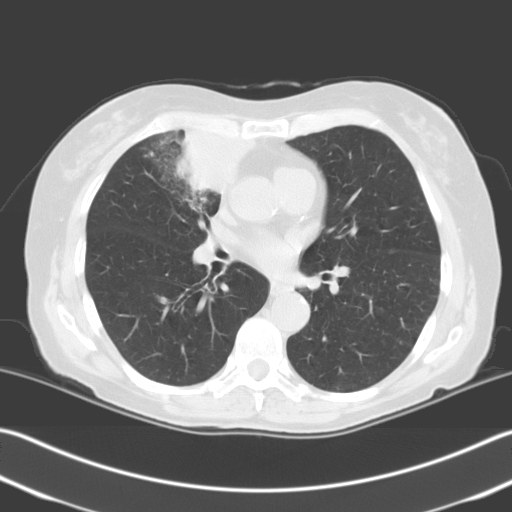
Low-dose screening chest CT, one axial slice; slice 116 of 204 in the series (ordered by position); lung window (W 1500 / L -600 HU); 3.2 mm slice thickness; 512 × 512 image matrix, field of view 348 × 348 mm.
Annotated regions visible in this slice (expert manual segmentation):
- lesion 1 (tumor, upper lobe of right lung): bounding box [x1, y1, x2, y2] px = [176, 131, 252, 195]